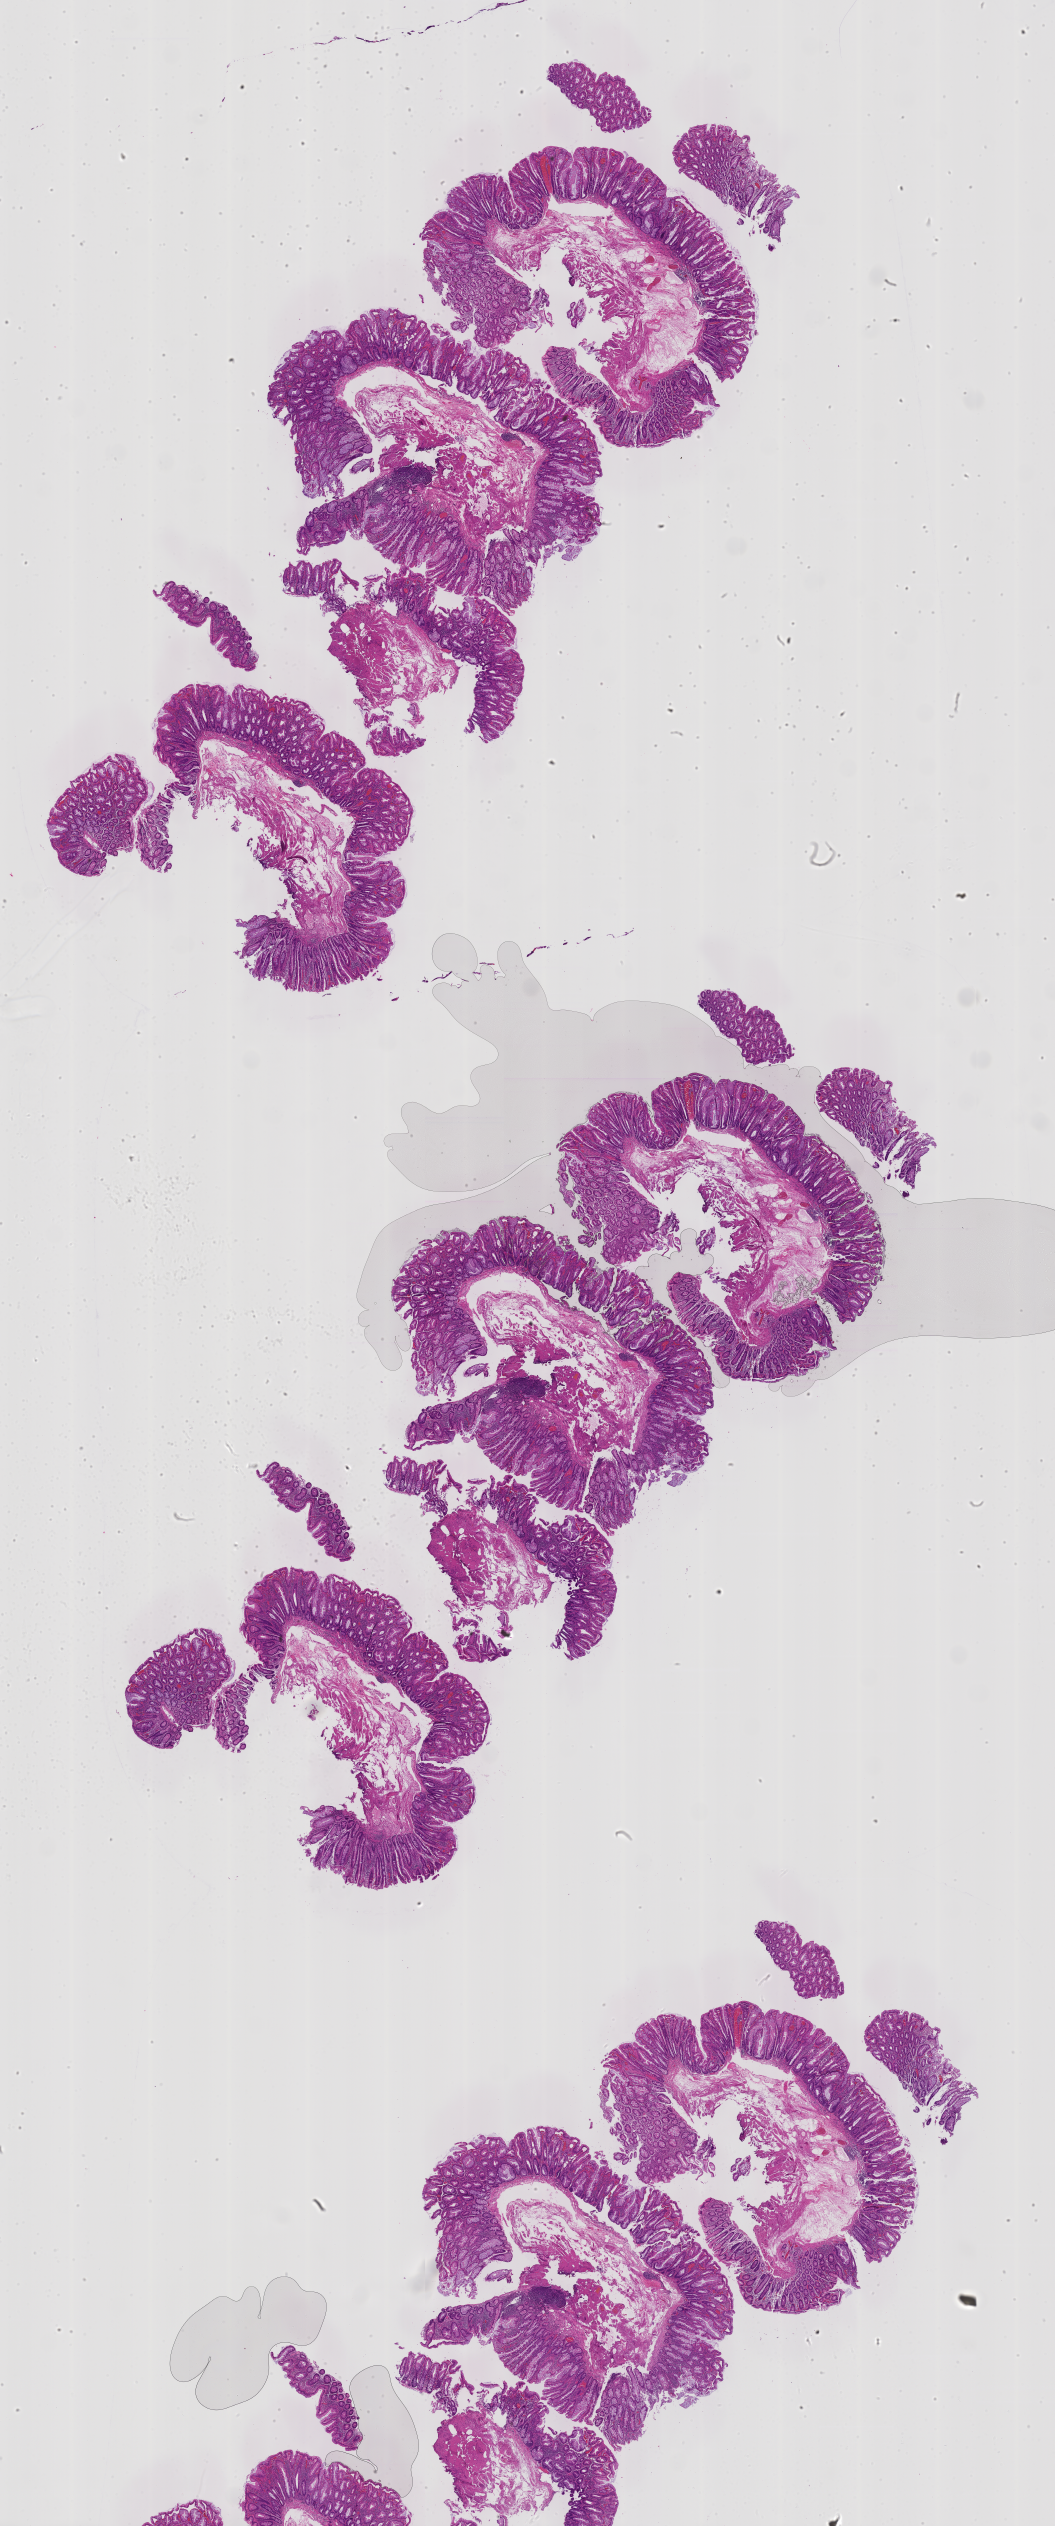
Whole-slide image, H&E stain: colon biopsy — shown as a low-resolution overview of the whole scanned area (about 16.9 x 40.4 mm). FFPE section. Cecum. Patient sex: male.
Lesion category (as recorded): premalignant.